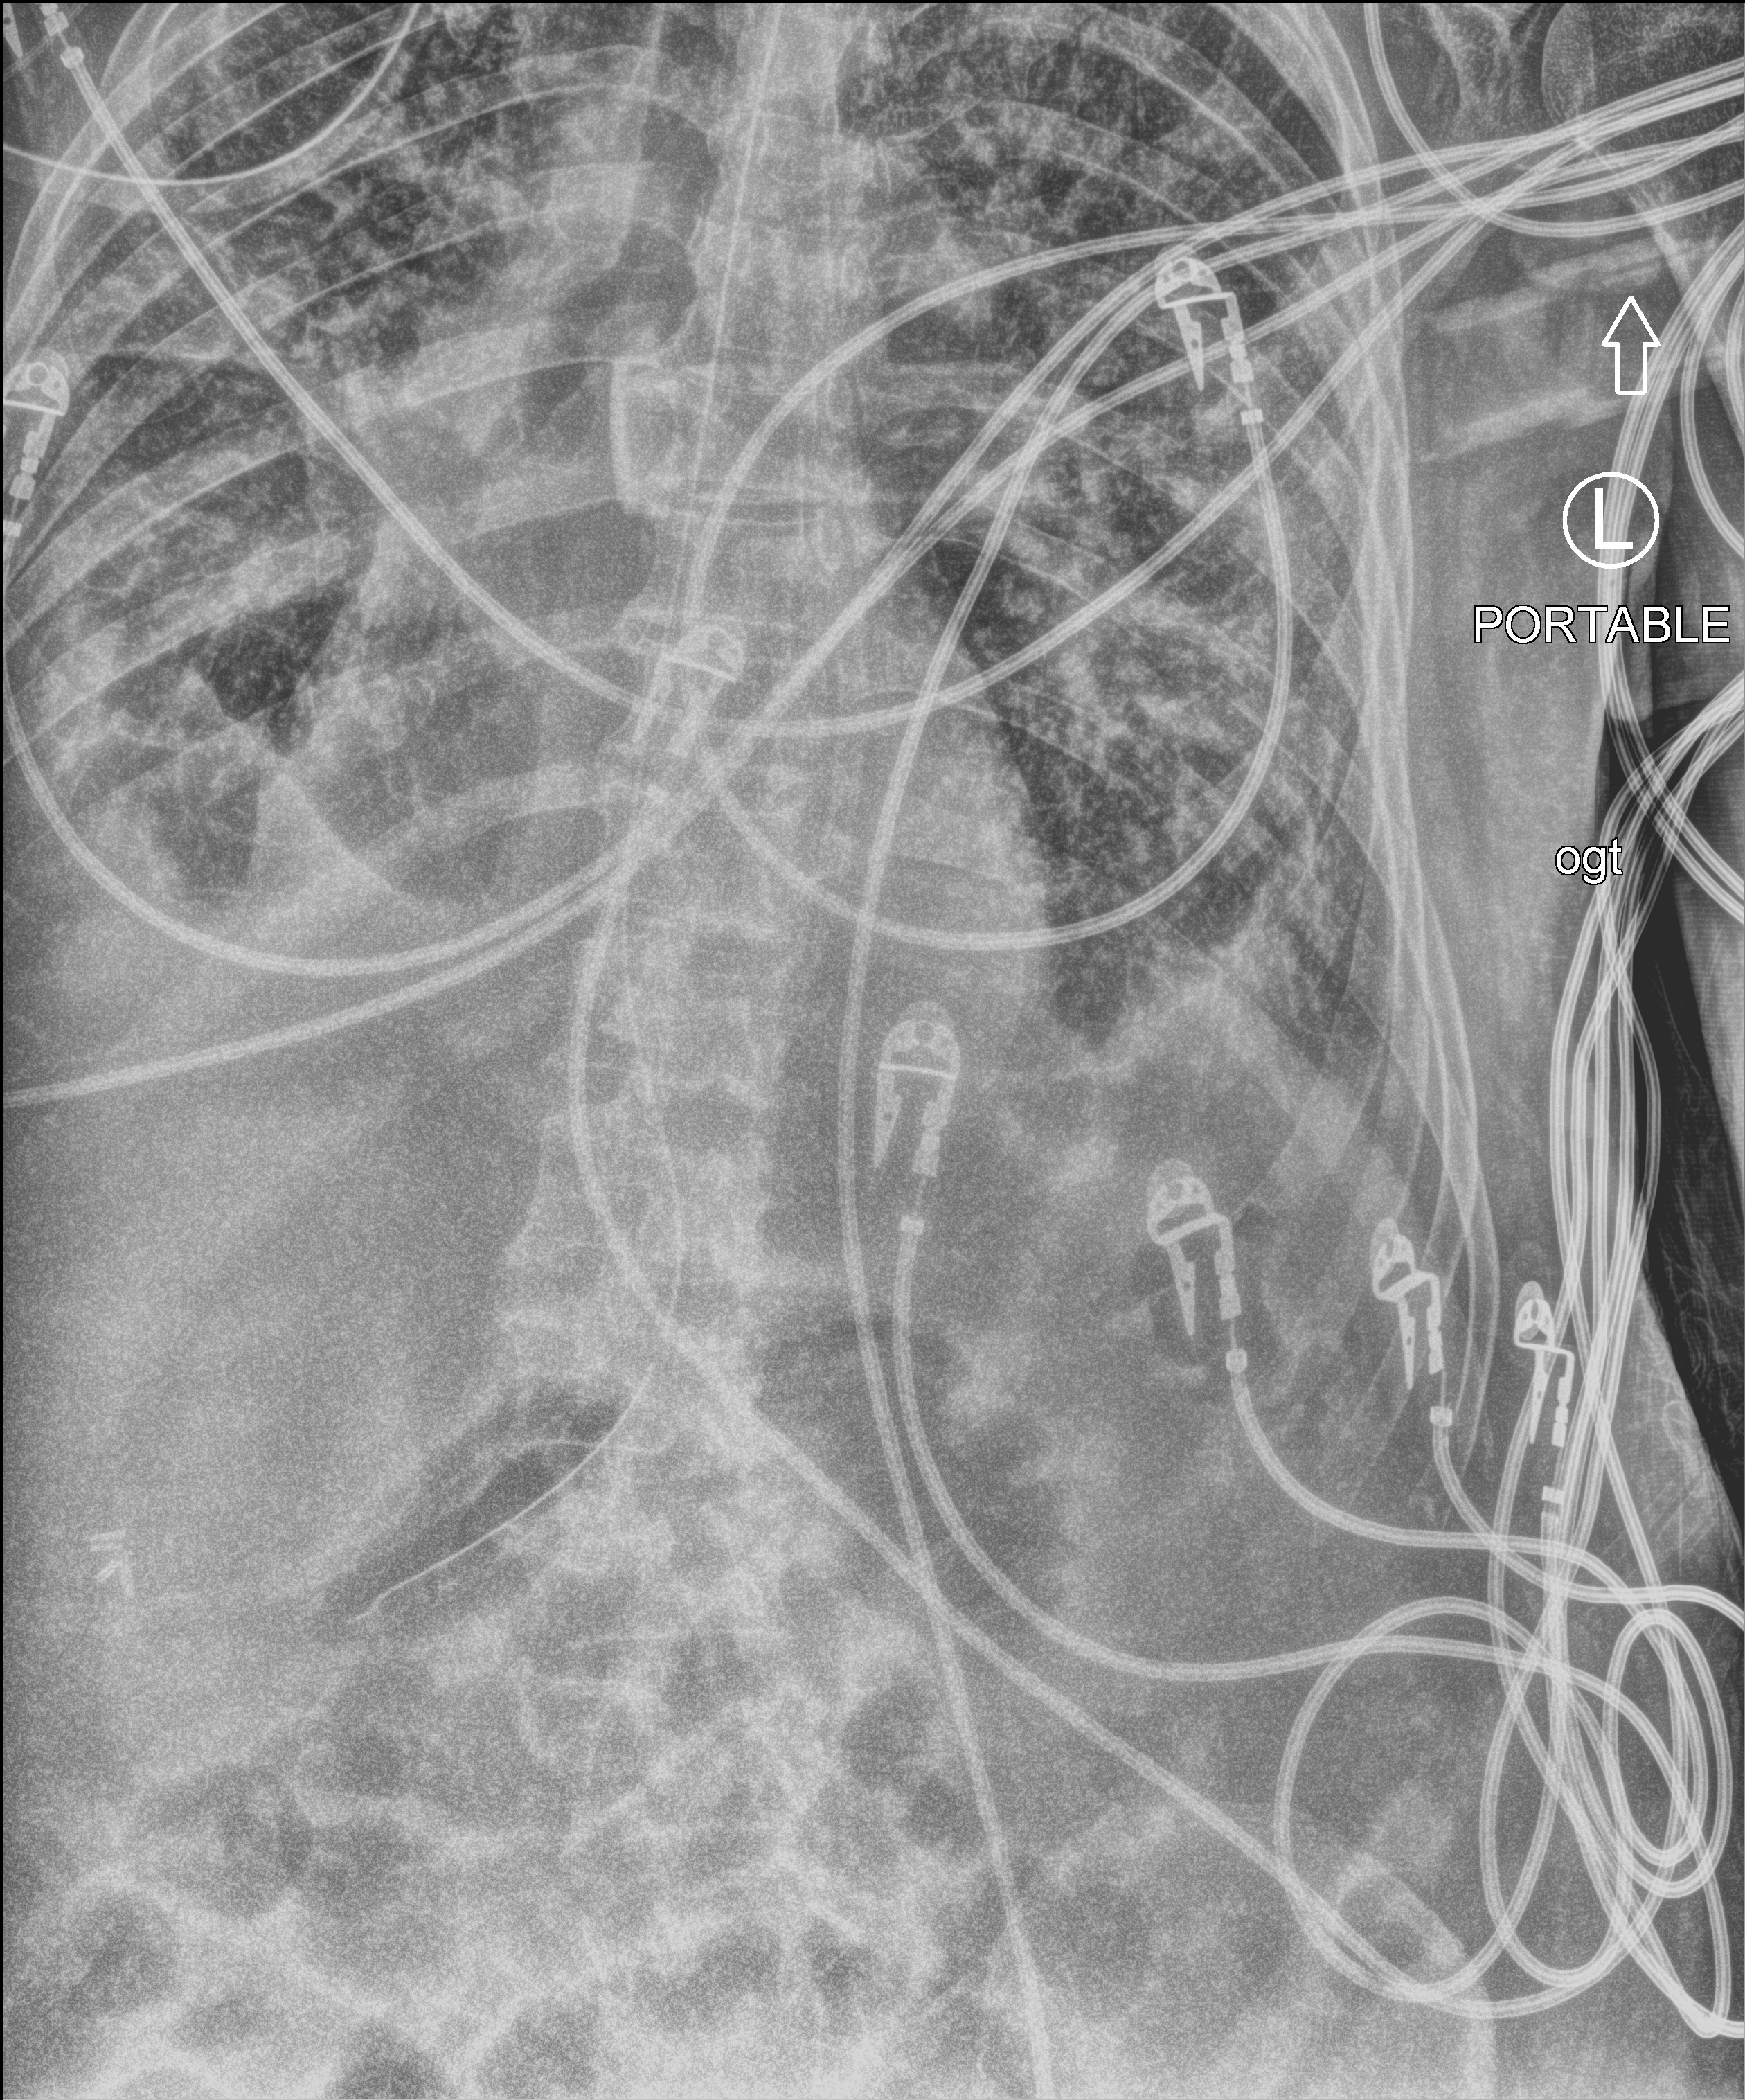
Chest X-ray (portable), anteroposterior (AP) projection. Patient hospitalised with COVID-19; male, aged 75–90 years.
Admission-level facts for this patient (not findings on this image; timing relative to this image not recorded): admitted to intensive care during this hospital stay: yes.